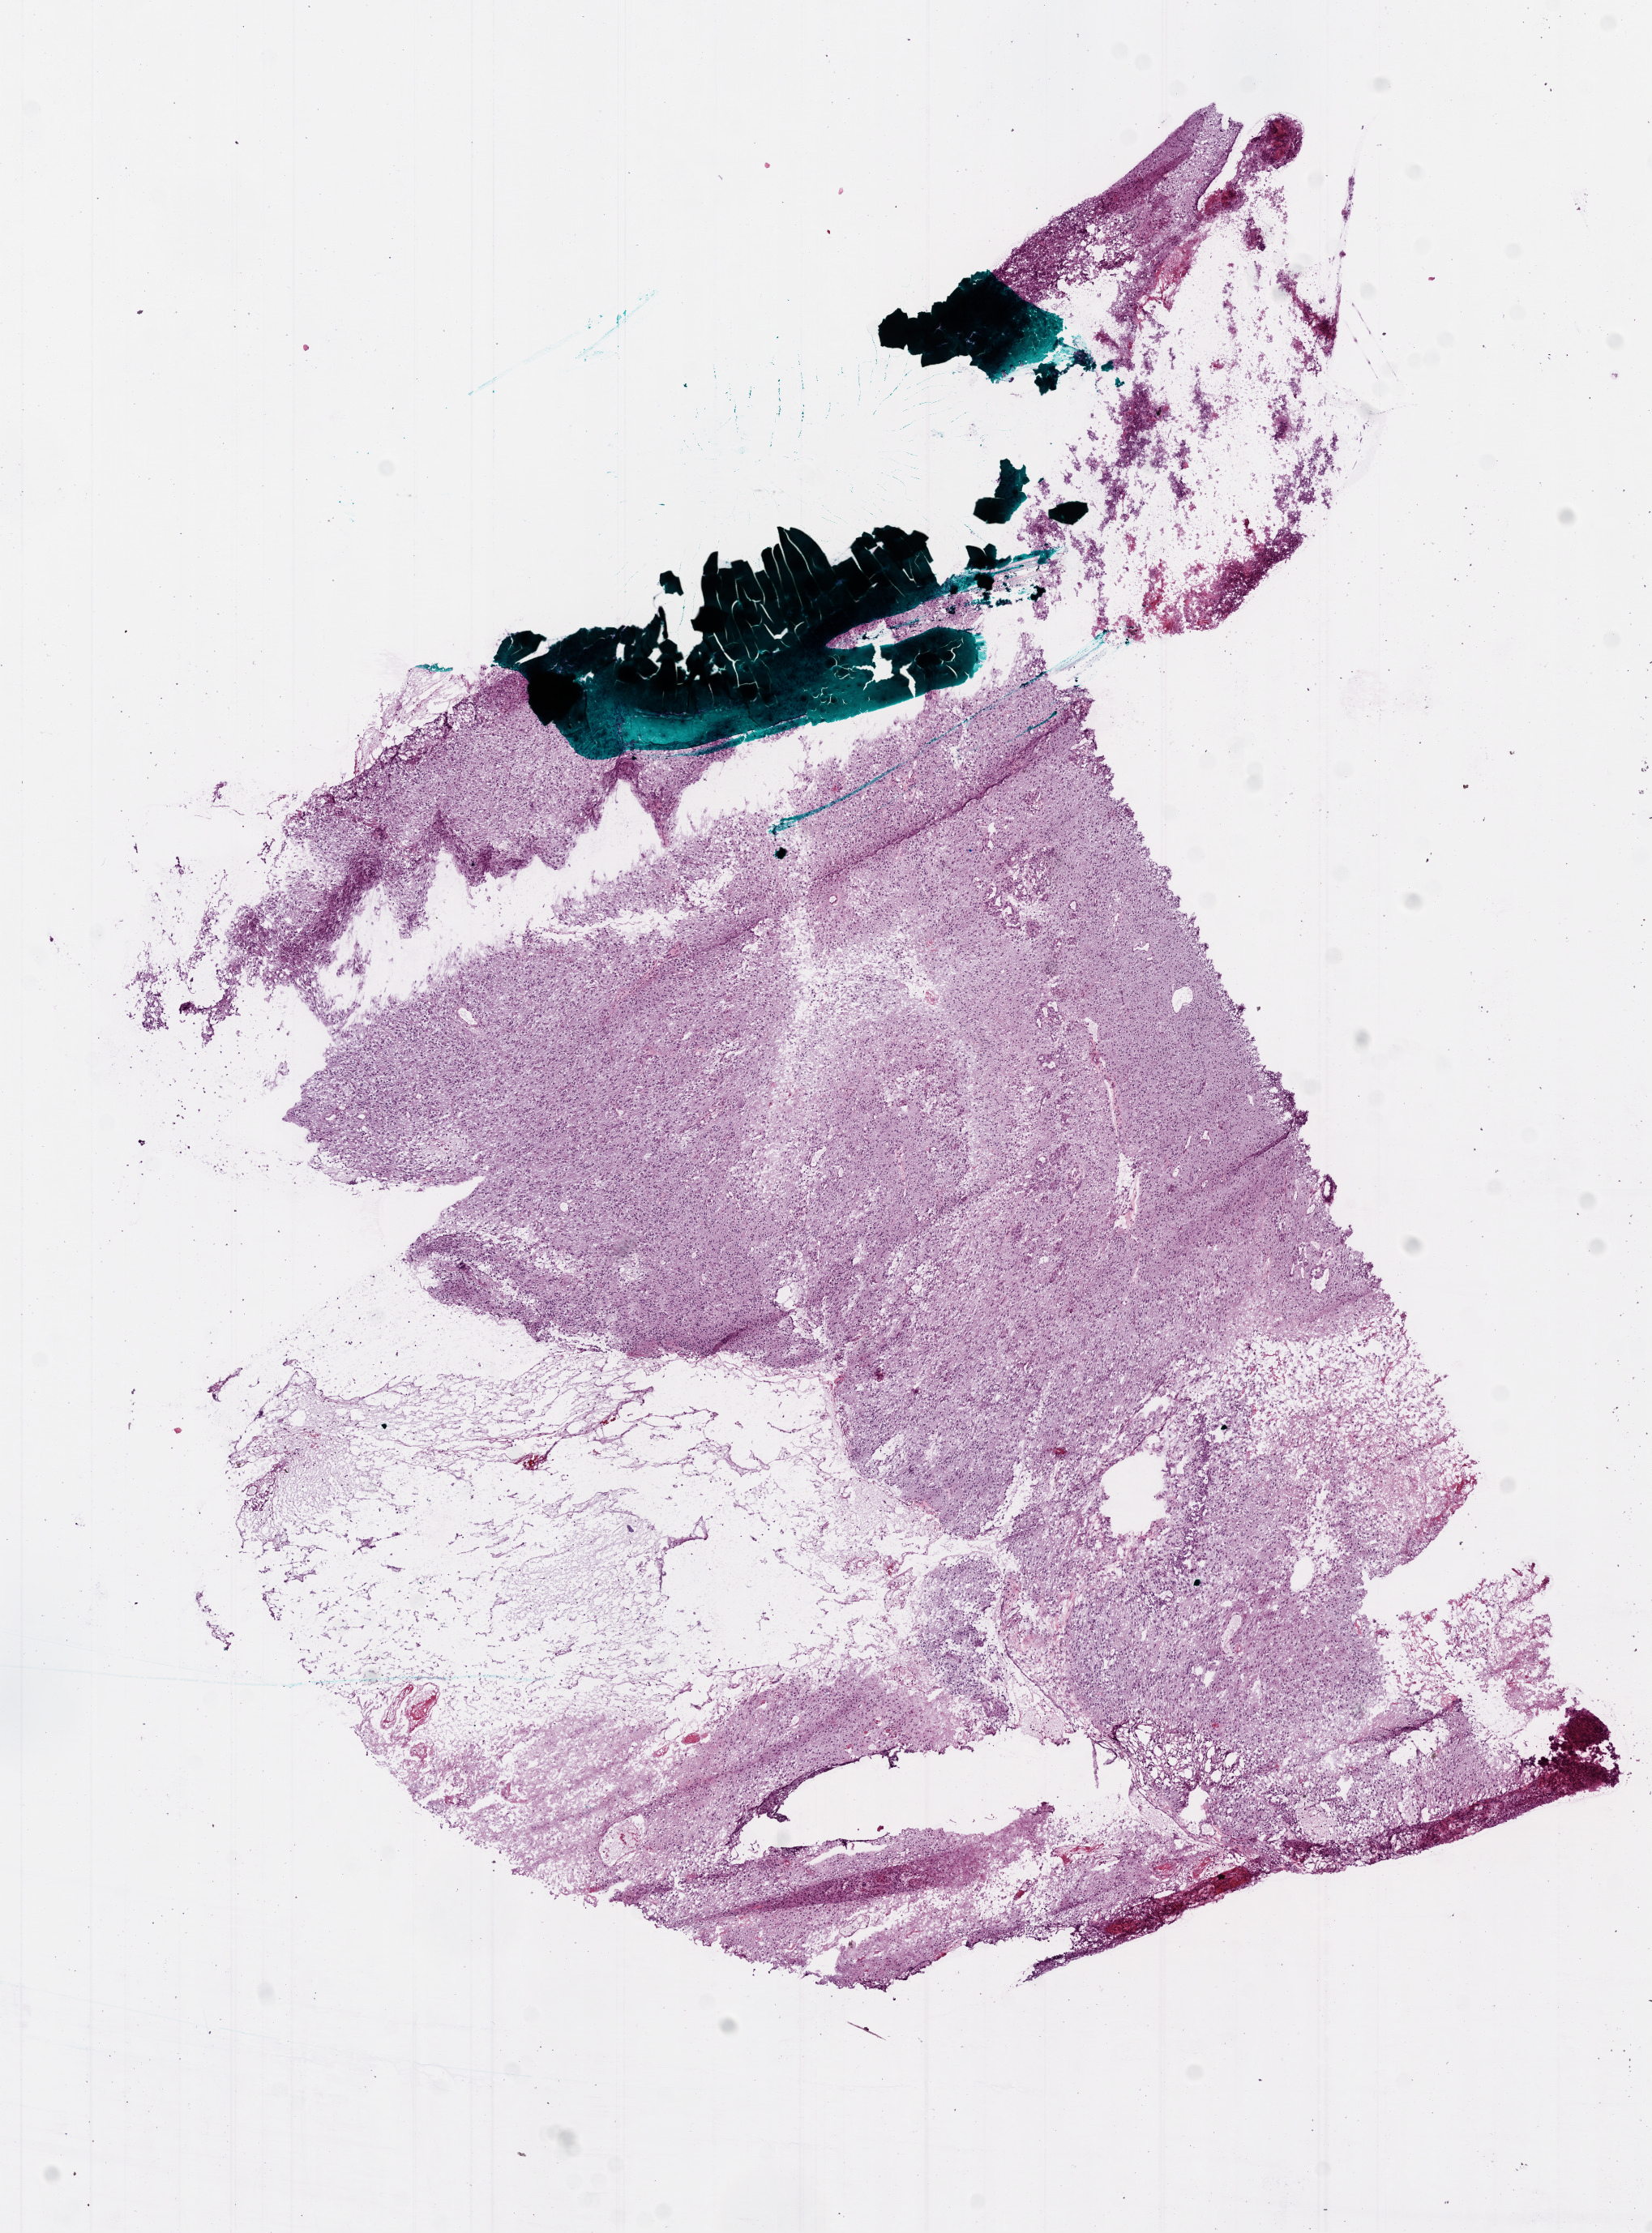
Digitized Hematoxylin and eosin (H&E) stained tissue section (whole slide), low-resolution overview of the scanned area, about 8.2 x 11.1 mm (acquisition: 20x scan), frozen section from the bottom of the tissue portion, brain, primary tumour sample. Male patient; age at initial diagnosis 70 years. Slide review estimates, as recorded: tumour cells 70%, tumour nuclei 90%, normal cells 0%, stromal cells 5%, necrosis 25%.
• histologic diagnosis: Glioblastoma